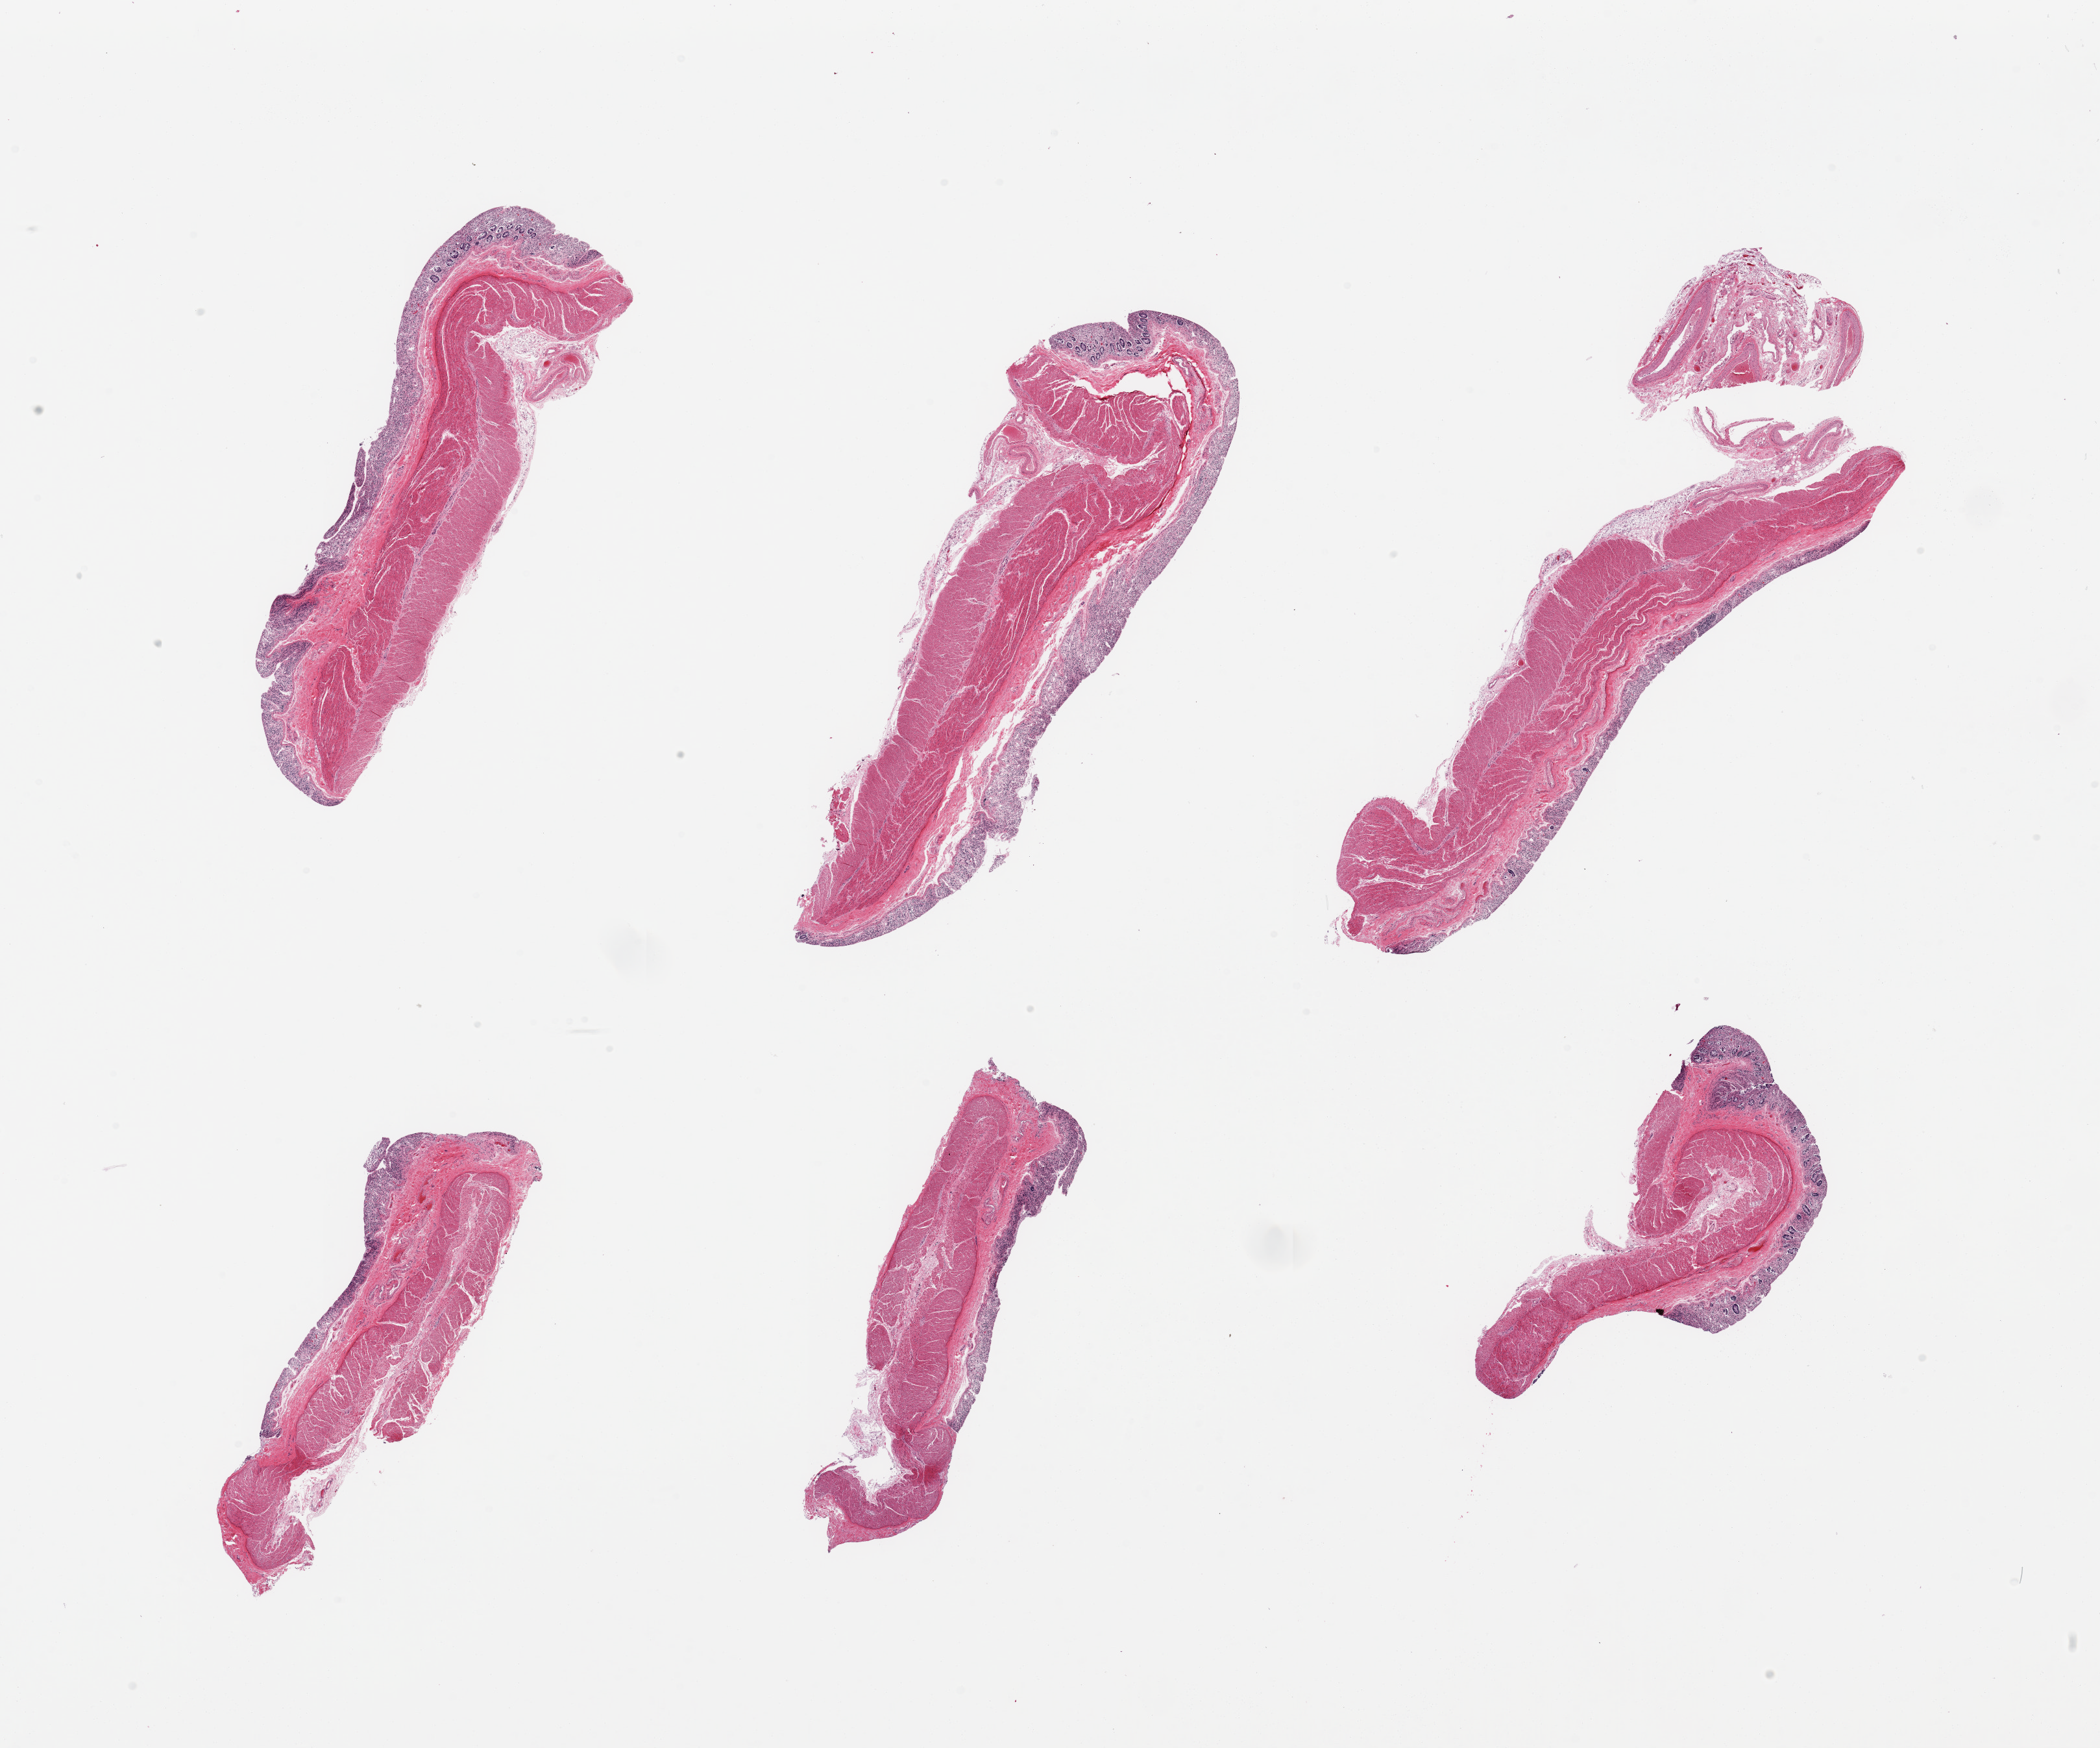
H&E whole-slide image, shown as a low-resolution overview of the whole scanned area (about 25.6 x 21.3 mm, from a 20x scan). PAXgene-fixed paraffin-embedded (PFPE) section. Target tissue: transverse colon. Donor tissue sample. Male donor.
Reviewer comment on this tissue sample: 6 pieces, target muscosa up to ~0.6mm, ~5-10% of thickness, glandular elements totally autolyzed.